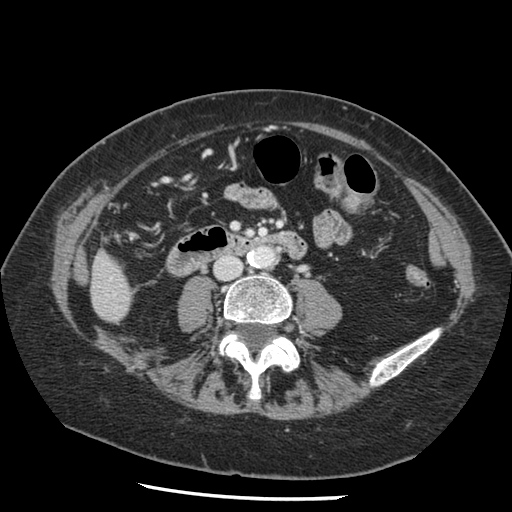
Contrast-enhanced abdominal CT, one axial slice; slice 20 of 148 in the series (ordered by position); reconstruction kernel STANDARD; 120 kVp; intravenous contrast given; soft-tissue window (W 400 / L 40 HU); 2.5 mm slice thickness; 512 × 512 image matrix, field of view 330 × 330 mm. Female patient, age 85 years. Case-level facts recorded for this patient, not image findings: diagnosis: colorectal cancer liver metastases, imaged before liver resection; multiple liver metastases: no; largest metastasis: 0.9 cm; disease in both lobes: no.
Annotated regions visible in this slice (expert manual segmentation):
- liver: box from (x=91, y=255) to (x=131, y=322) px
- planned liver remnant (the part of the liver to remain after resection): (x=91, y=255)–(x=131, y=321)